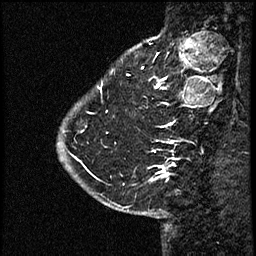
Breast MRI (dynamic contrast-enhanced), one sagittal slice; slice 13 of 60 in the series (ordered by position); dynamic contrast-enhanced study with each time point stored as its own series, time point 2 of 4 at this slice position (early post-contrast, ordered by acquisition time); 1.5 T; TE 4.2 ms, TR 17.6 ms; 256 × 256 image matrix. Female patient, age 43 years. From the clinical record (not read from this slice): setting: breast cancer imaged before/during neoadjuvant chemotherapy.
Annotated regions visible in this slice (semi-automatic segmentation, software-assisted and operator-edited):
- analysis volume of interest (the breast-tissue region the enhancement analysis was run in; not a lesion): bounding box <66,56,169,191> (left, top, right, bottom; pixels)
- tumour enhancement mask (voxels above the 100 % enhancement threshold inside the analysis volume of interest): <160,170,166,173>